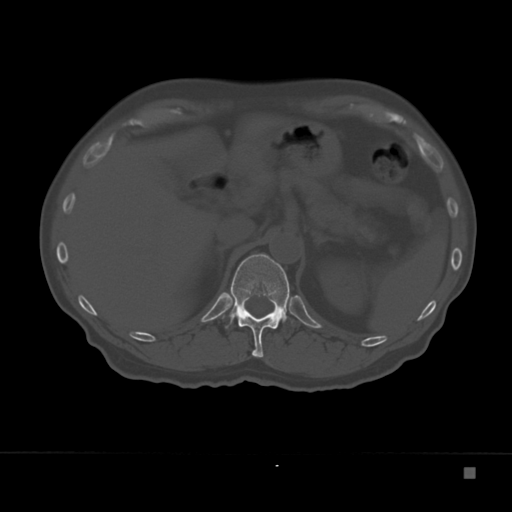
CT including the spine, one axial slice; slice 131 of 332 in the series (ordered by position); reconstruction kernel Br40s; bone window (W 1800 / L 400 HU); 1.5 mm slice thickness; 512 × 512 image matrix, field of view 389 × 389 mm. Patient: male, 72 years. Case-level facts recorded for this patient, not image findings: primary cancer: skeletal.
Outlined on this slice (semi-automatic segmentation, software-assisted and operator-edited):
- T12 vertebra: bounding box <223,253,291,358> (left, top, right, bottom; pixels)